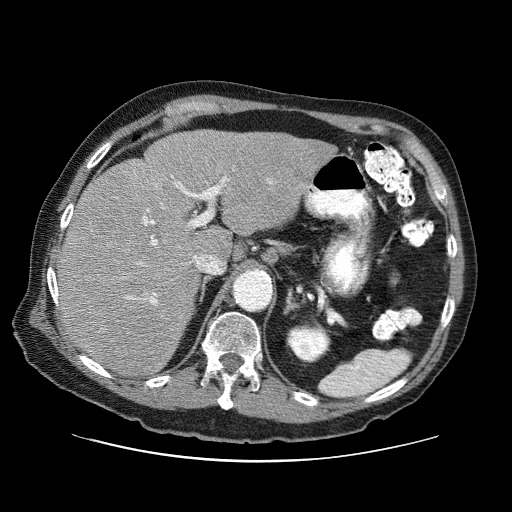
Contrast-enhanced abdominal CT (liver protocol), one axial slice. Position 48 of 87 along the scan axis. Reconstruction kernel STANDARD. 120 kVp. One of 3 acquisitions stored at this slice position. Soft-tissue window (W 400 / L 40 HU). 2.5 mm slice thickness. 512 × 512 image matrix, field of view 400 × 400 mm. From the clinical record (not read from this slice): diagnosis: hepatocellular carcinoma (patient treated with transarterial chemoembolisation; whether this scan precedes or follows treatment is not stated here); TNM stage (as recorded): Stage-IIIA; Child-Pugh class: A; tumour differentiation: well differentiated.
Structures marked on this image (semi-automatically segmented with operator editing):
- liver parenchyma outside the tumour (the mass and vessels are separate outlines, so this box may not span the whole liver): bounding box <58,130,335,376> (left, top, right, bottom; pixels)
- liver vessels: <127,176,271,304>